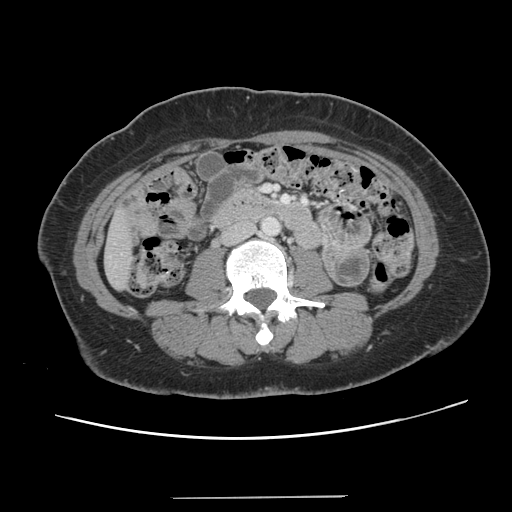
Contrast-enhanced abdominal CT, one axial slice; slice 24 of 141 in the series (ordered by position); 120 kVp; intravenous contrast given; soft-tissue window (W 400 / L 40 HU); 2.5 mm slice thickness; 512 × 512 image matrix, field of view 366 × 366 mm. Female patient, age 53 years. From the clinical record (not read from this slice): diagnosis: colorectal cancer liver metastases, imaged before liver resection; multiple liver metastases: no; largest metastasis: 14.5 cm; chemotherapy before resection: yes.
Outlined on this slice (manually delineated by an expert):
- liver: bounding box <105,213,134,289> (left, top, right, bottom; pixels)
- planned liver remnant (the part of the liver to remain after resection): <106,214,134,289>